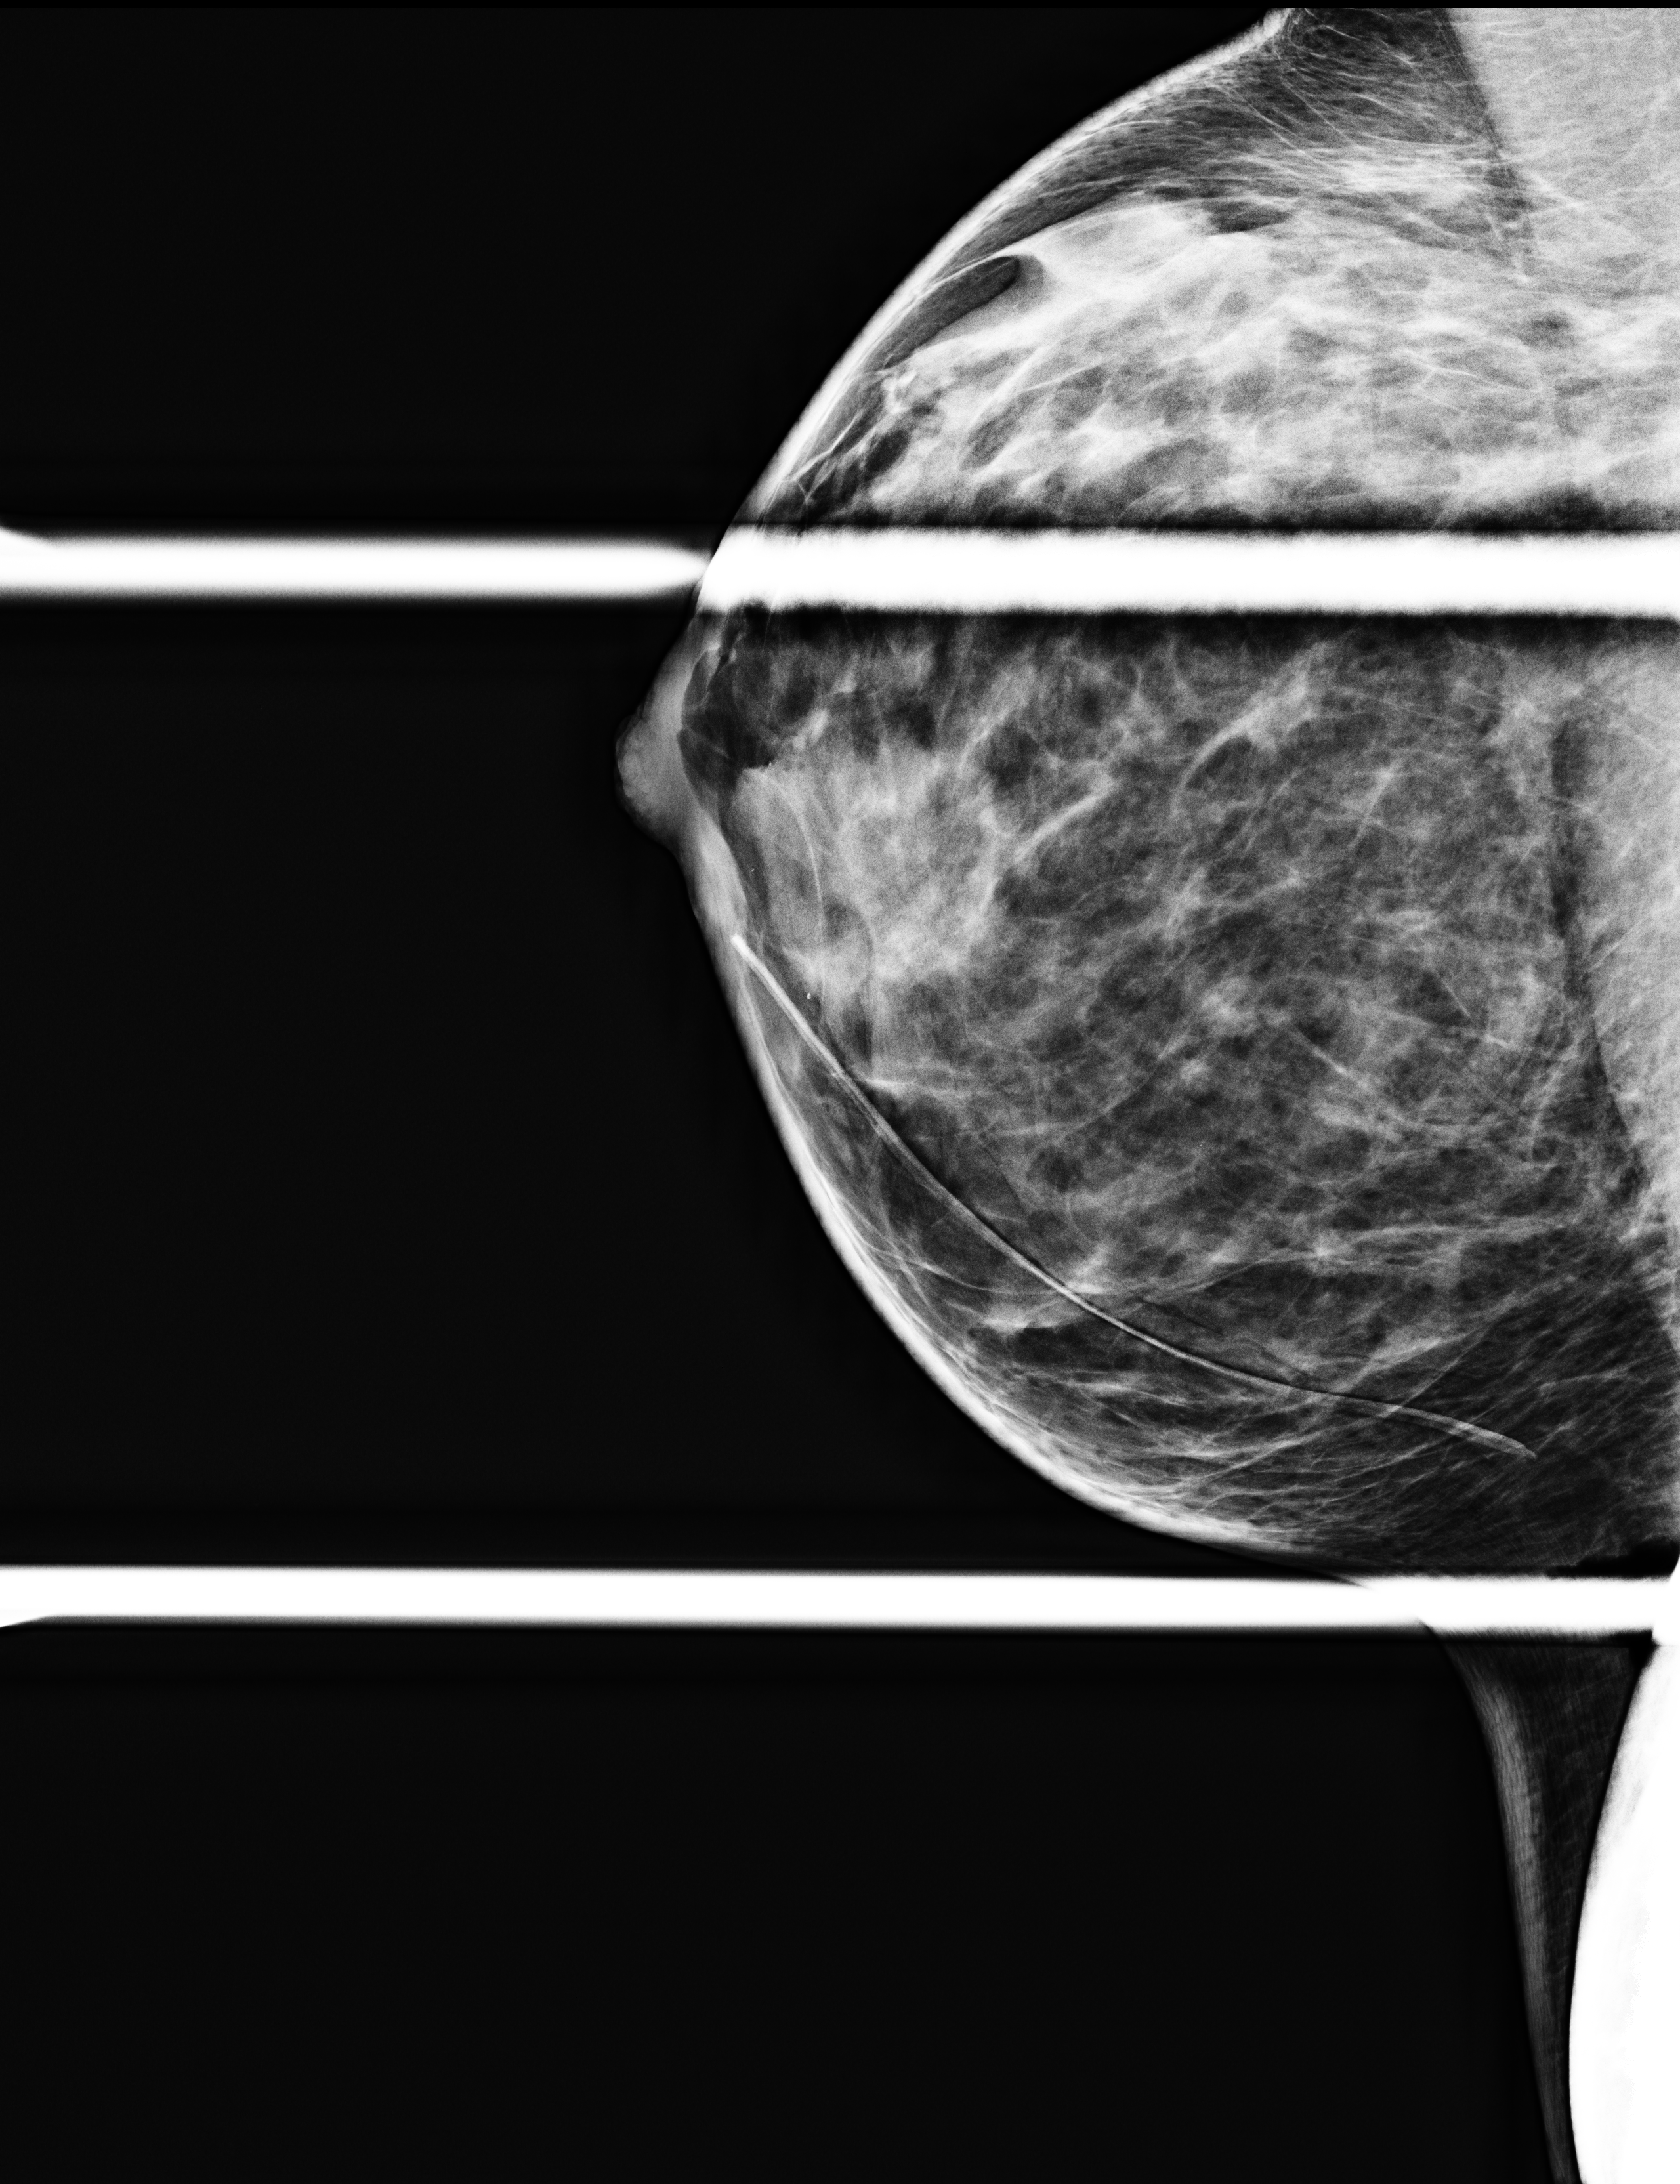
Additional (diagnostic) view; compressed breast thickness 33 mm; system: Selenia Dimensions. Female patient, age 44 years.
Image type: full-field digital mammogram. Breast: right. Projection: mediolateral oblique (MLO) view, spot compression.